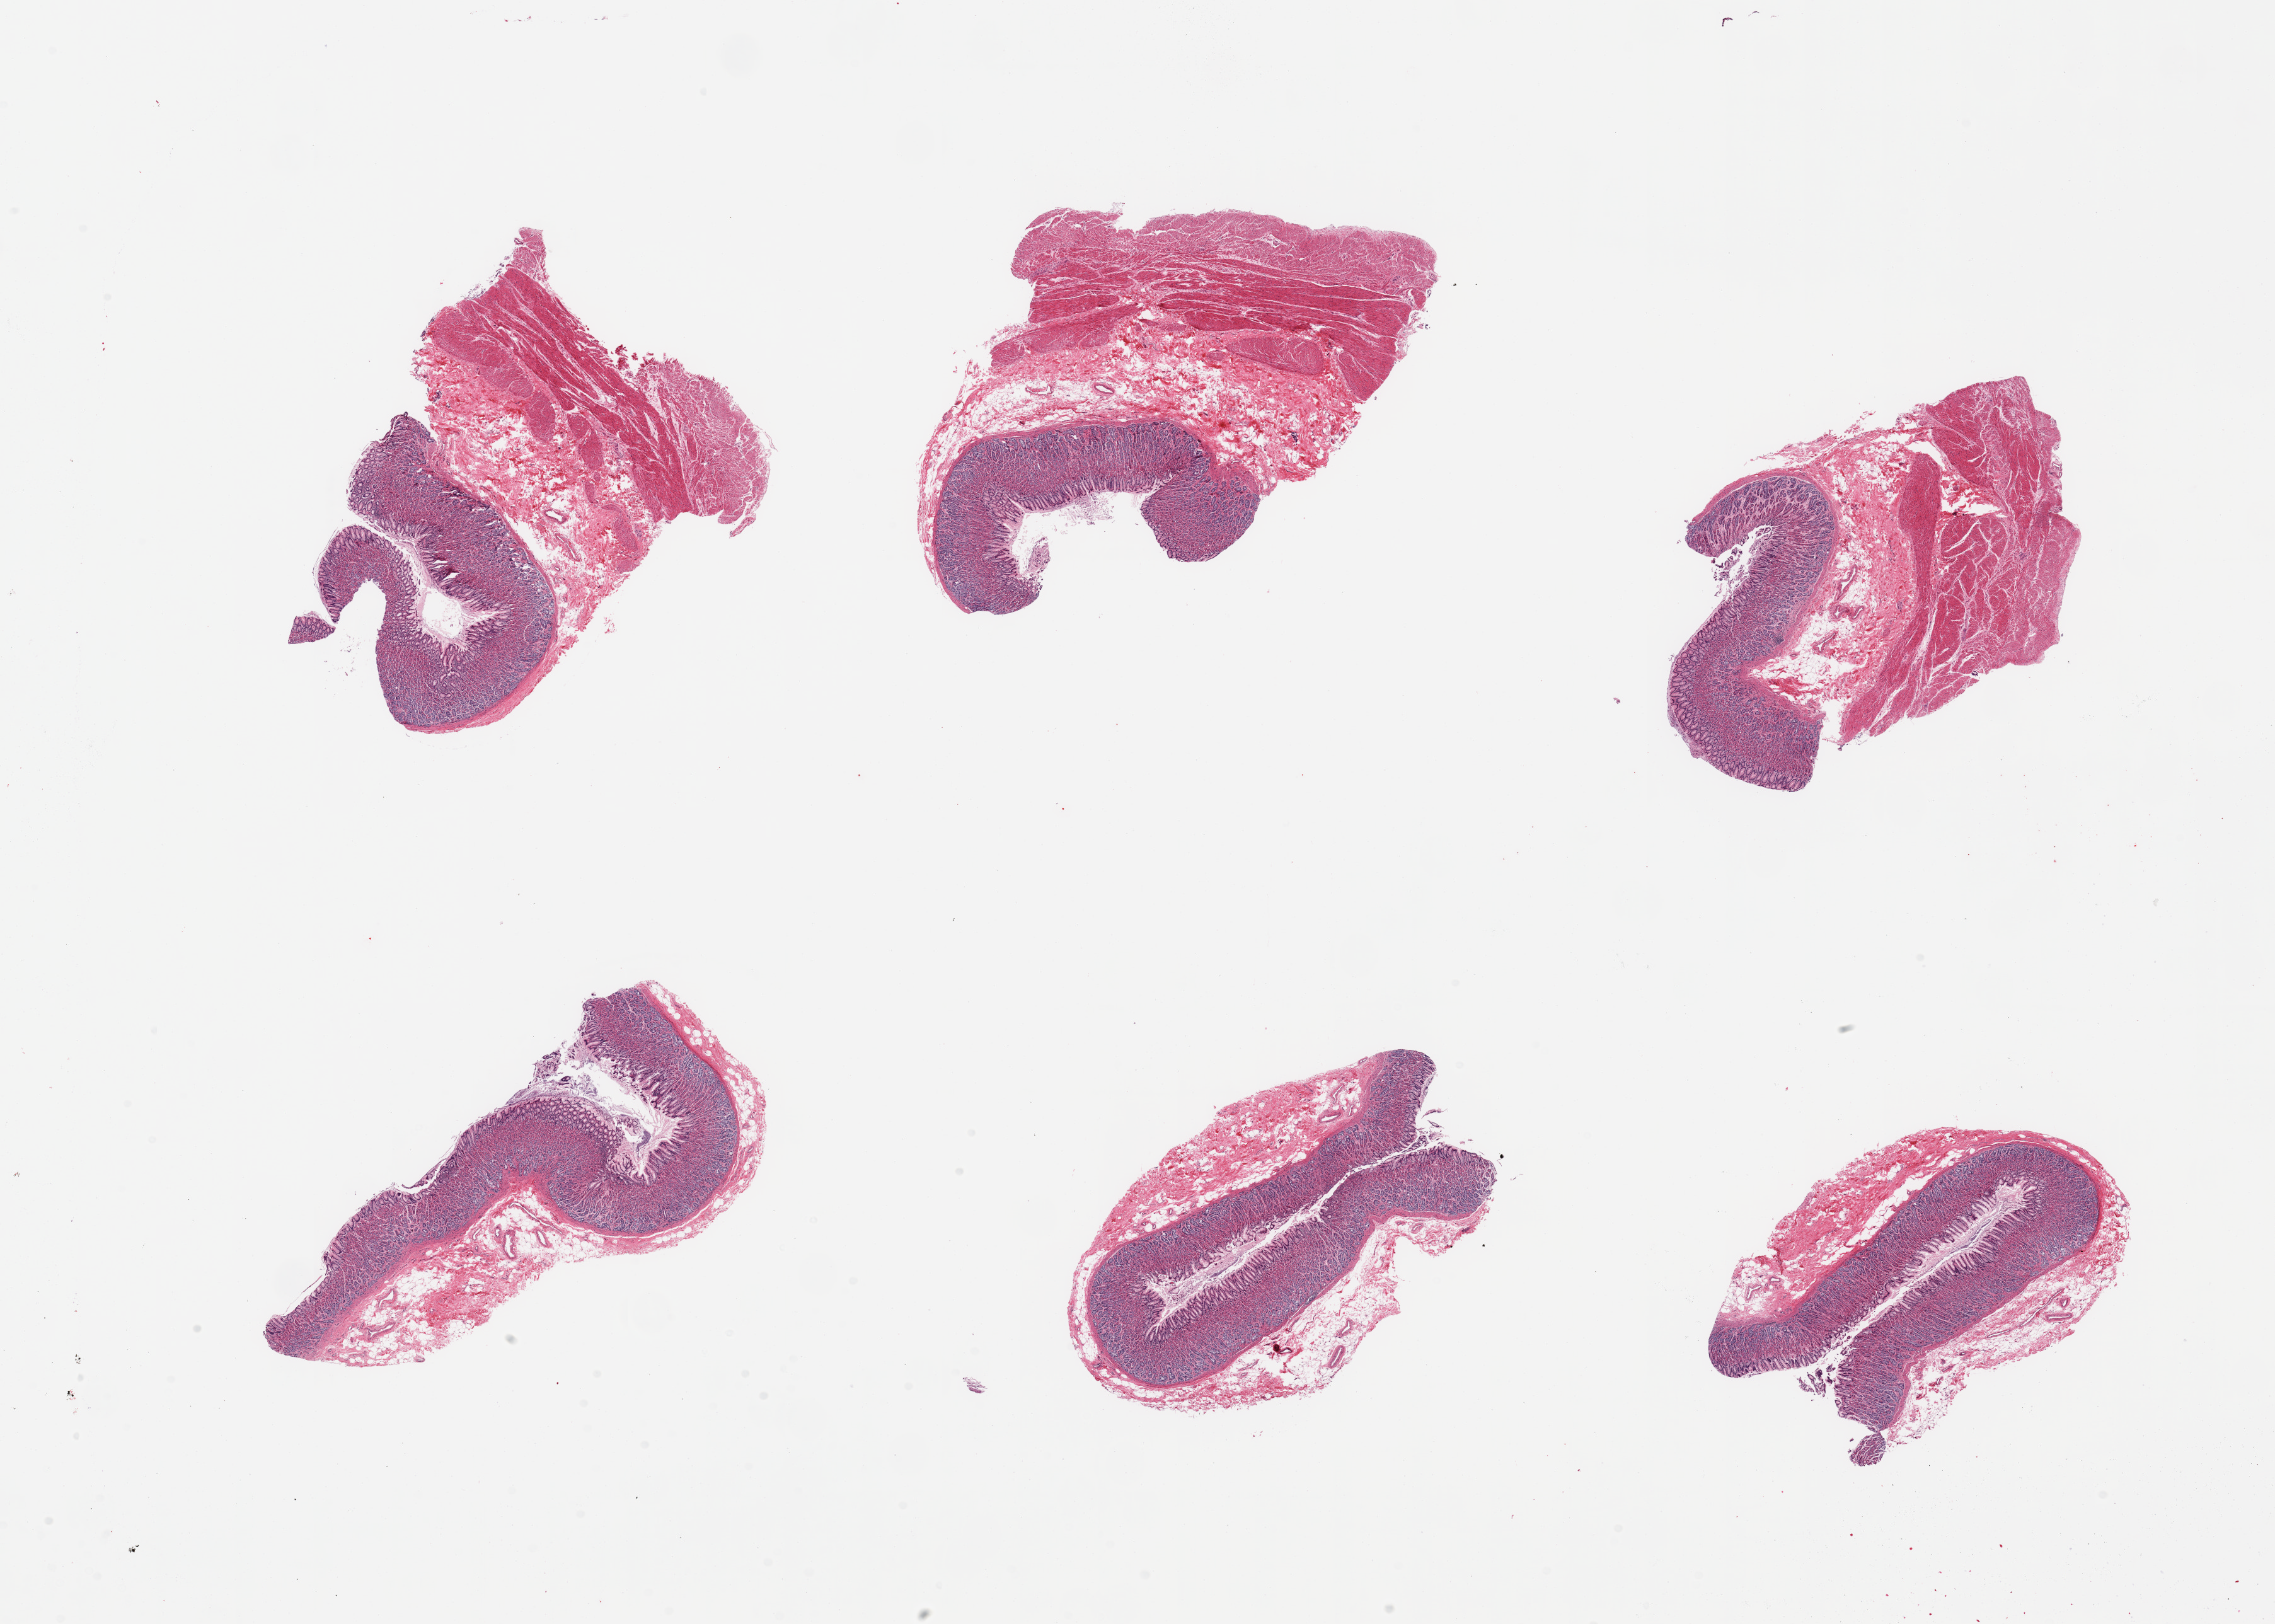
Whole-slide image, H&E stain, brightfield, shown as a low-resolution overview of the whole scanned area (about 28.5 x 20.4 mm, from a 20x scan); PAXgene-fixed, paraffin-embedded tissue; section of stomach (target tissue); donor tissue sample.
Pathologist's review note for this sample: 6 pieces; 3 include mucosa and muscularis, 3 are mucosa only.